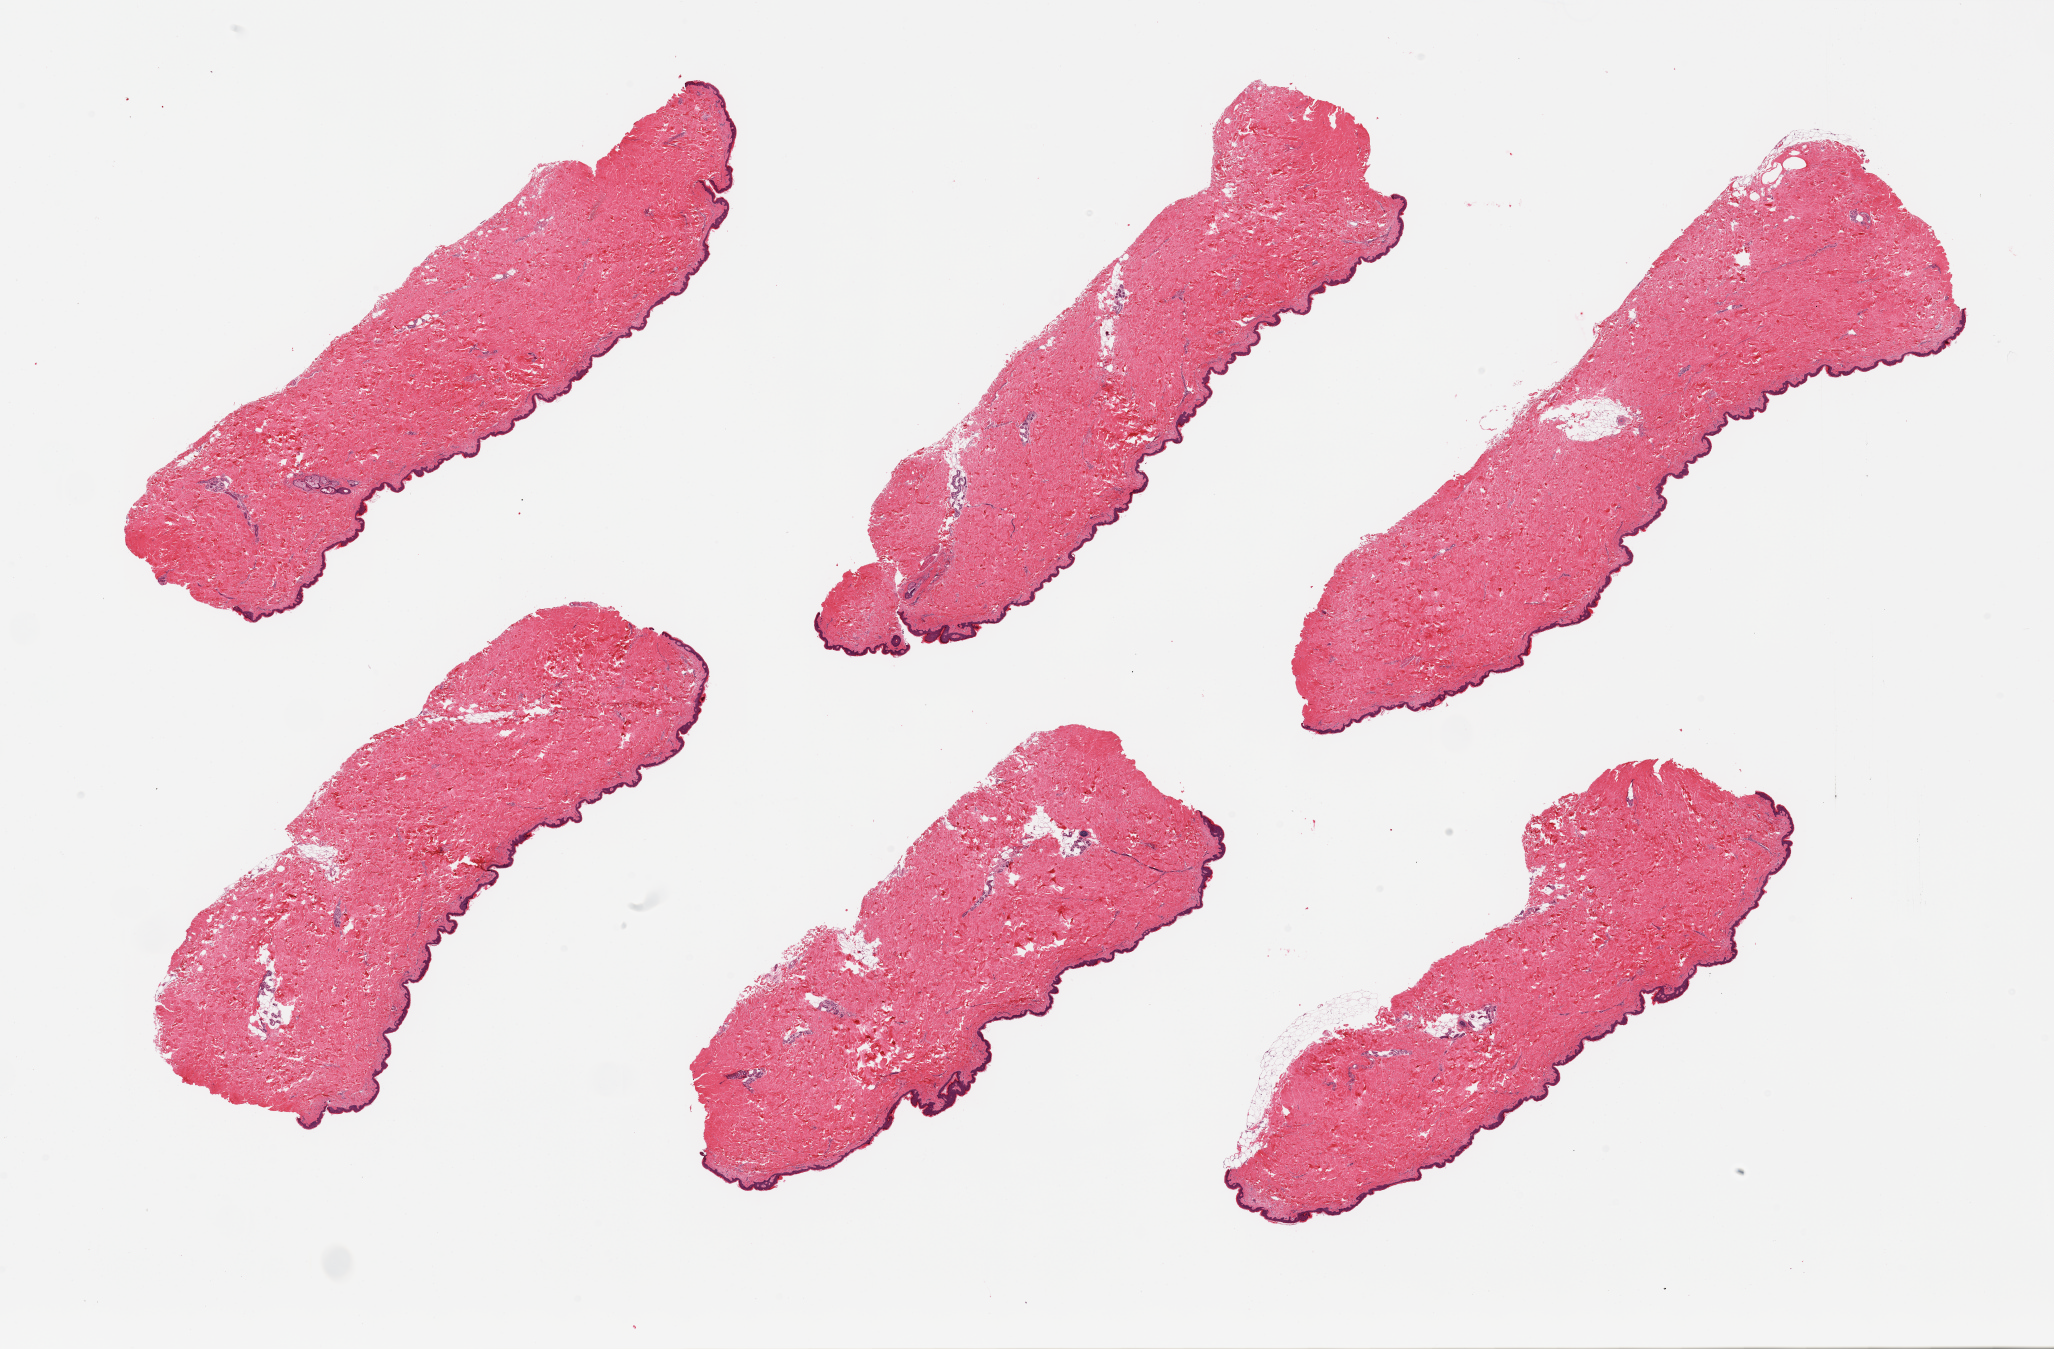
Haematoxylin and eosin whole-slide image, brightfield, a low-resolution overview of the entire scanned area, about 32.5 x 21.3 mm (slide scanned at 20x); PAXgene-fixed, paraffin-embedded tissue; target tissue: skin of suprapubic region; donor tissue sample. Female donor.
Review note (as recorded): pieces.